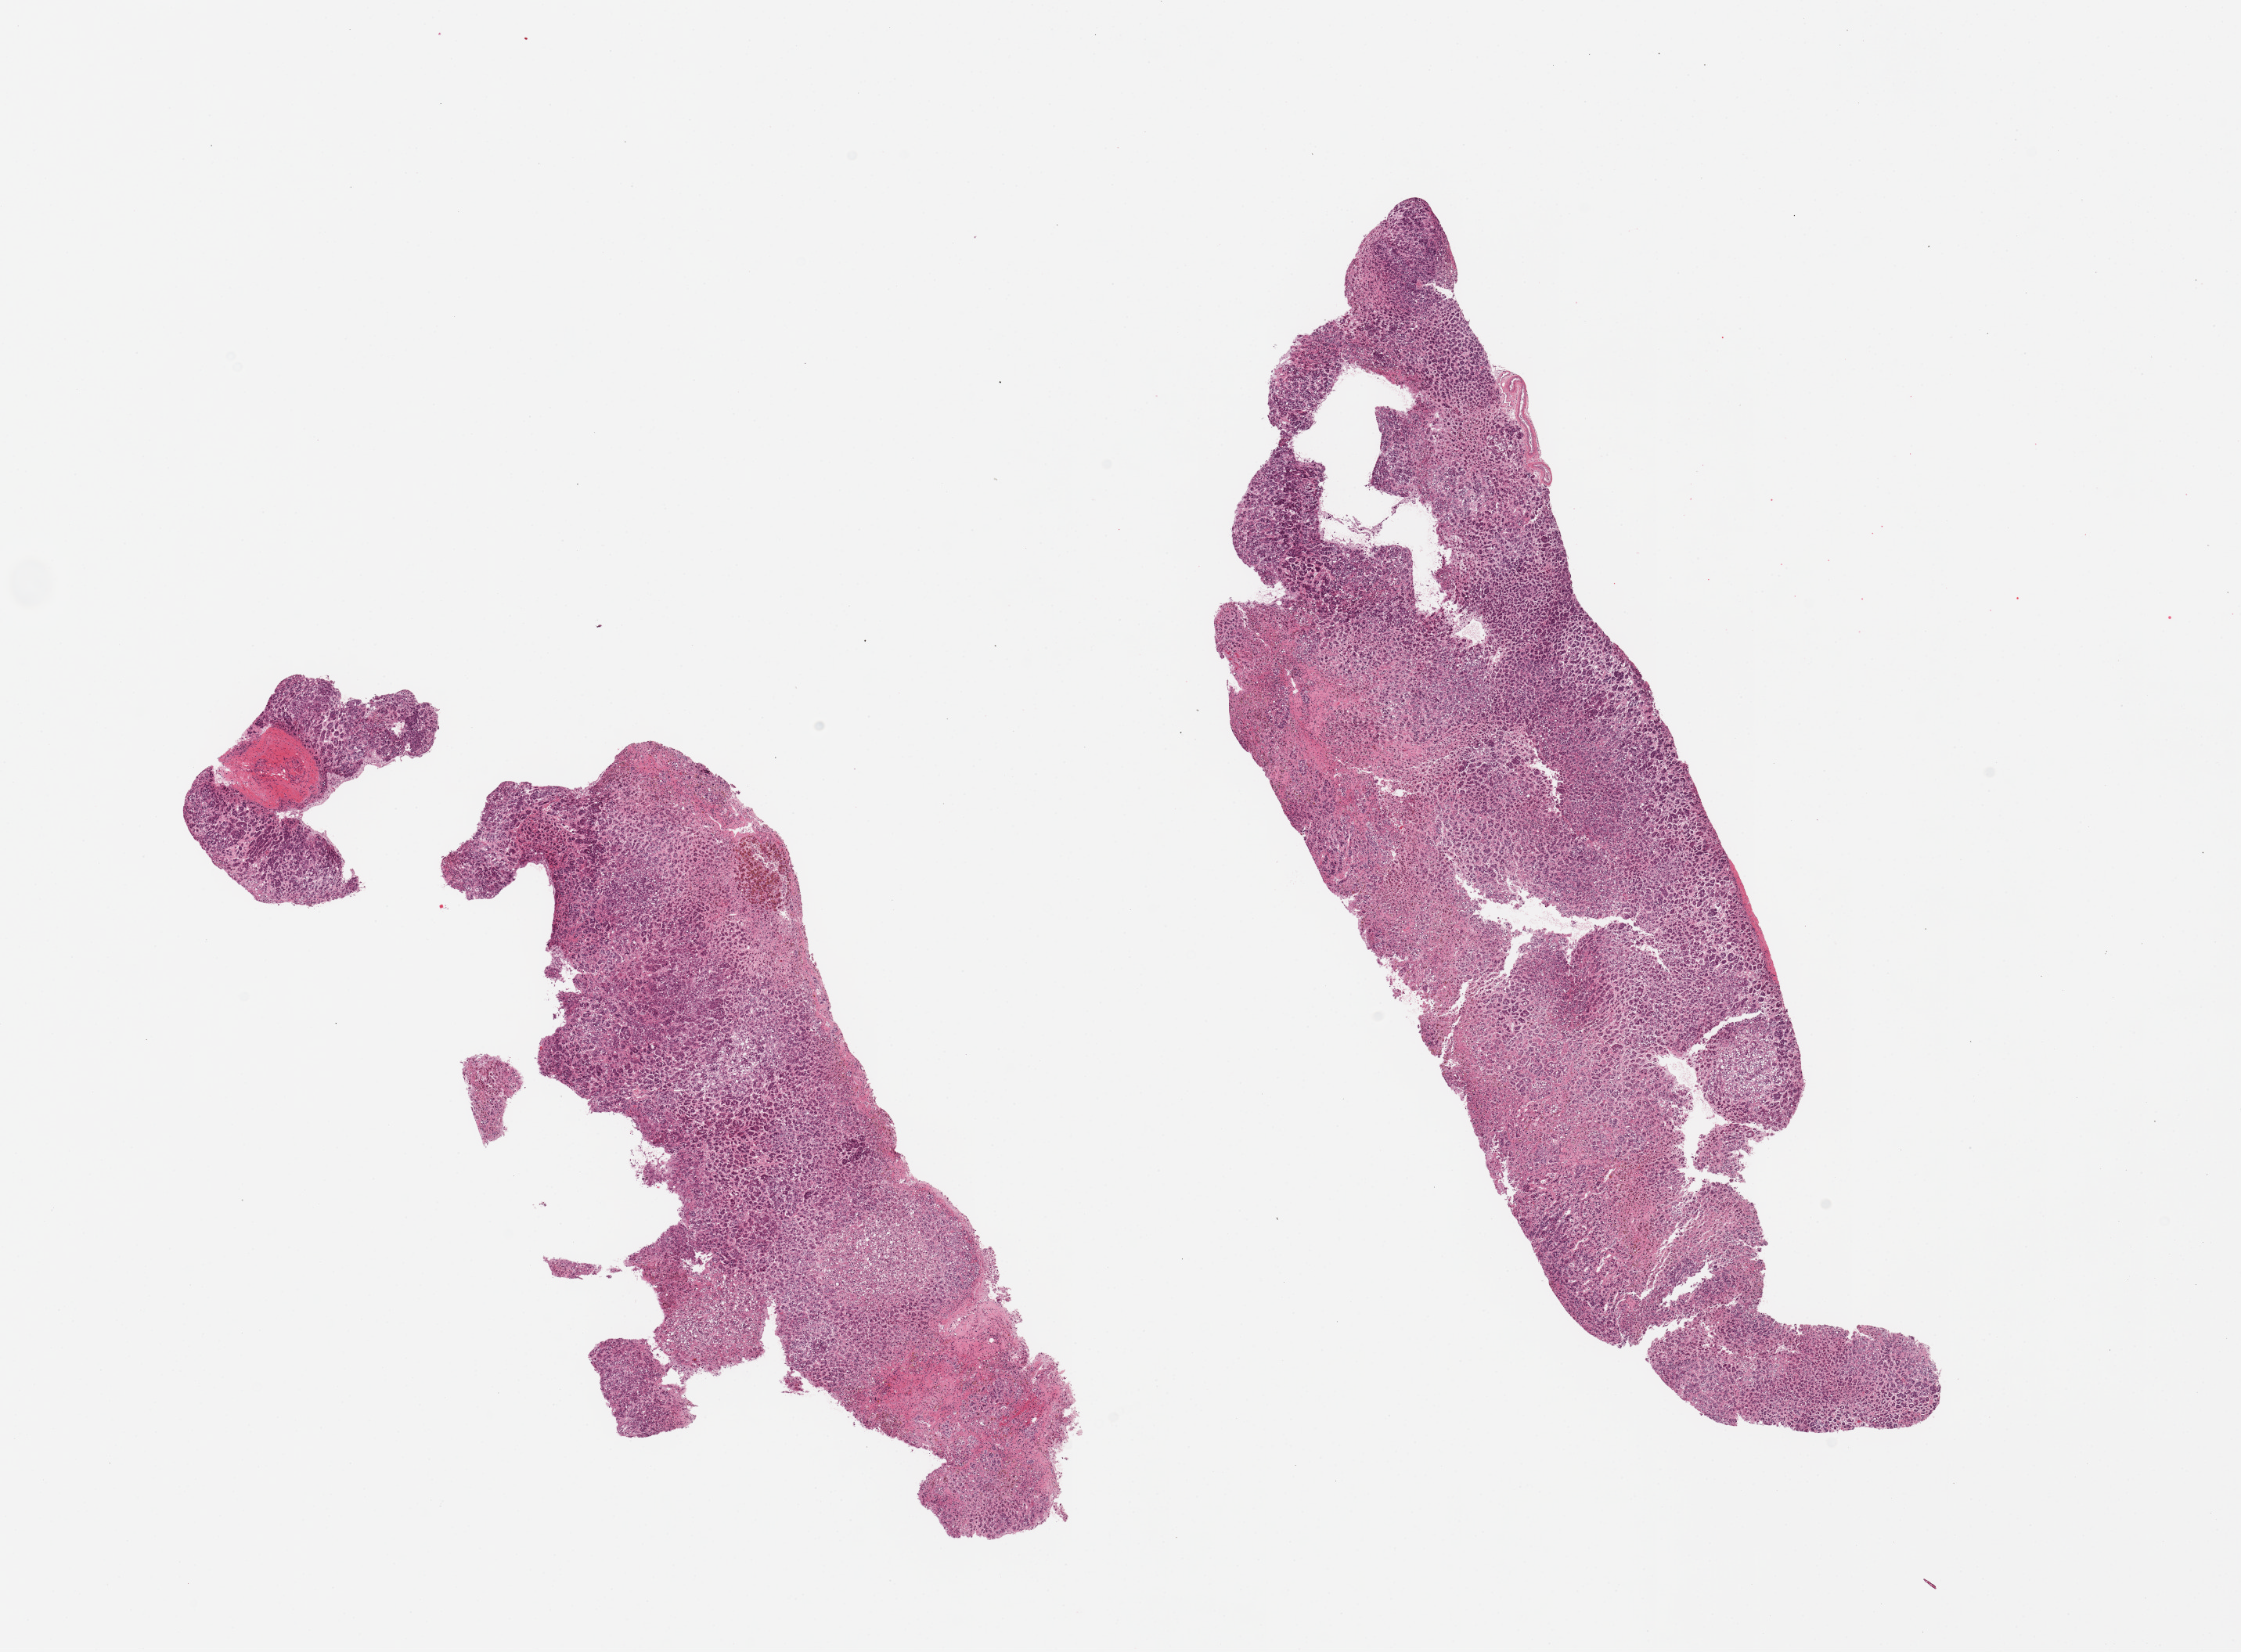
H&E whole-slide image — low-resolution overview of the scanned area, about 22.6 x 16.7 mm. PAXgene-fixed paraffin-embedded (PFPE) section. Section of adrenal gland (target tissue). Tissue donor sample.
Pathologist's review note for this sample: 2 pieces.